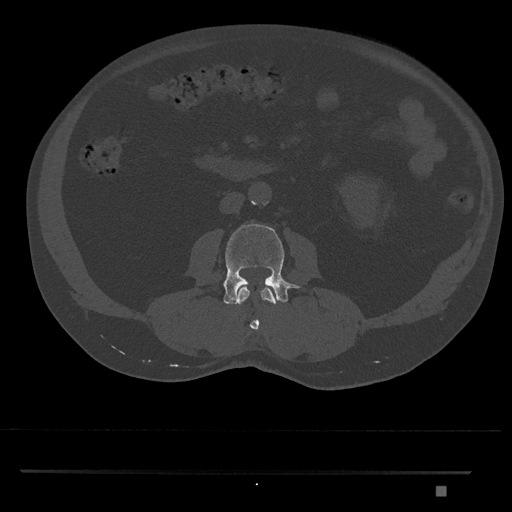
CT including the spine, one axial slice. Slice 702 of 1134 in the series (ordered by position). Reconstruction kernel Br40s/3. 120 kVp. Bone window (W 1800 / L 400 HU). 0.5 mm slice thickness. 512 × 512 image matrix, field of view 429 × 429 mm. Male patient, age 65 years. From the clinical record (not read from this slice): primary cancer: prostate.
Structures marked on this image (semi-automatic segmentation, software-assisted and operator-edited):
- L2 vertebra: bounding box <237,287,276,330> (left, top, right, bottom; pixels)
- L3 vertebra: <223,224,299,305>